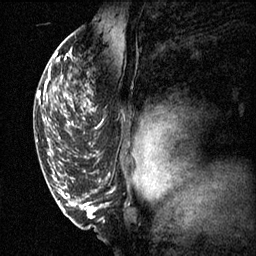
Breast MRI (dynamic contrast-enhanced), one sagittal slice. Slice 41 of 60 in the series (ordered by position). 3 images stored at this slice position (order not interpretable as contrast timing). 1.5 T. TE 4.2 ms, TR 11.1 ms. 2 mm slice thickness. 256 × 256 image matrix, field of view 180 × 180 mm. Patient: female, 50 years.
Outlined on this slice (semi-automatically segmented with operator editing):
- analysis volume of interest (the breast-tissue region the enhancement analysis was run in; not a lesion): box from (x=68, y=68) to (x=103, y=141) px
- tumour enhancement mask (voxels above the 70 % enhancement threshold inside the analysis volume of interest): (x=68, y=94)–(x=94, y=127)